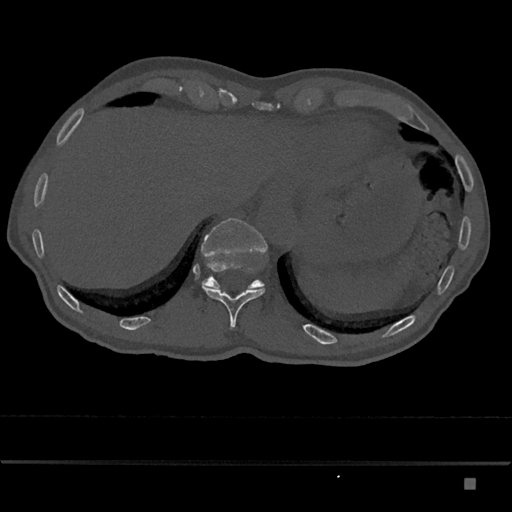
CT including the spine, one axial slice; position 655 of 797 along the scan axis; bone window (W 1800 / L 400 HU); 512 × 512 image matrix, field of view 390 × 390 mm. Patient: male, 72 years. Case-level facts recorded for this patient, not image findings: primary cancer: prostate.
Outlined on this slice (semi-automatic segmentation, software-assisted and operator-edited):
- T11 vertebra: bounding box [x1, y1, x2, y2] px = [202, 283, 265, 328]
- T12 vertebra: [201, 218, 267, 290]